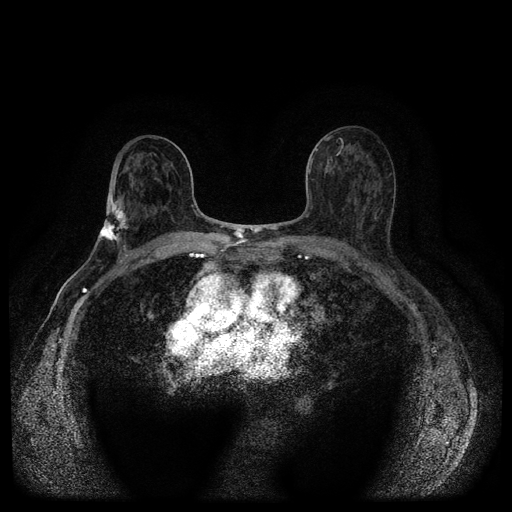
Breast MRI (dynamic contrast-enhanced, multi-phase), one axial slice; position 59 of 116 along the scan axis; dynamic contrast-enhanced series, time point 2 of 5 at this slice position (early post-contrast); 1.5 T; TE 2.7 ms, TR 5.4 ms; 2 mm slice thickness; 512 × 512 image matrix. Patient: female, 75 years.
Structures marked on this image (semi-automatically segmented with operator editing):
- breast lesion (labelled 'tumour' in the annotation; benign lesions carry a separate 'benign' label): bounding box (x1, y1, x2, y2) in pixels: (99, 195, 132, 242)